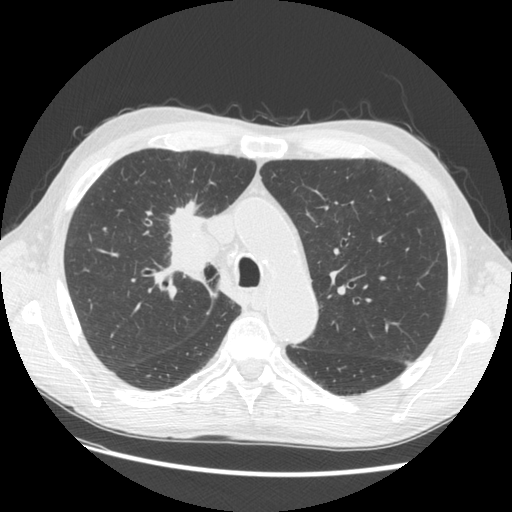
Low-dose screening chest CT, one axial slice. Position 95 of 133 along the scan axis. Reconstruction kernel STANDARD. Lung window (W 1500 / L -600 HU). 2.5 mm slice thickness. 512 × 512 image matrix, field of view 360 × 360 mm.
Annotated regions visible in this slice (outlined manually by an expert reader):
- lesion 1 (tumor, hilum of right lung): bounding box <169,199,220,283> (left, top, right, bottom; pixels)